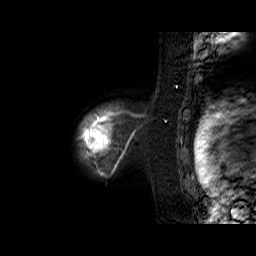
Breast MRI (dynamic contrast-enhanced), one sagittal slice; slice 55 of 60 in the series (ordered by position); dynamic contrast-enhanced series, time point 2 of 6 at this slice position (early post-contrast); 1.5 T; TE 6.3 ms, TR 32.9 ms; 4 mm slice thickness; 256 × 256 image matrix. Female patient. Case-level facts recorded for this patient, not image findings: setting: breast cancer imaged before/during neoadjuvant chemotherapy; receptor status: triple-negative.
Structures marked on this image (semi-automatically segmented with operator editing):
- analysis volume of interest (the breast-tissue region the enhancement analysis was run in; not a lesion): bounding box <78,105,143,170> (left, top, right, bottom; pixels)
- tumour enhancement mask (voxels above the 100 % enhancement threshold inside the analysis volume of interest): <78,107,132,170>